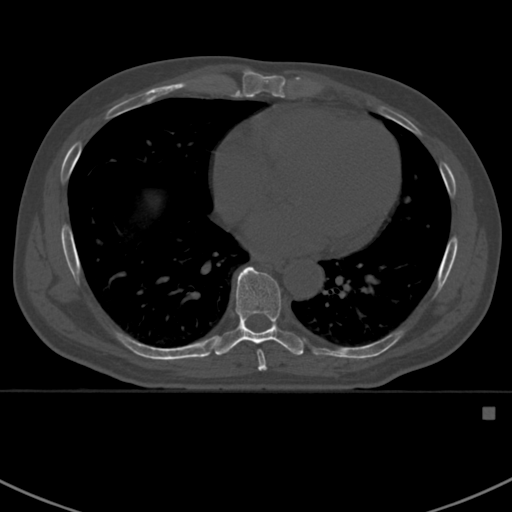
CT including the spine, one axial slice. Reconstruction kernel Br40s. 120 kVp. Bone window (W 1800 / L 400 HU). 512 × 512 image matrix, field of view 358 × 358 mm. Male patient, age 59 years. From the clinical record (not read from this slice): primary cancer: prostate.
Structures marked on this image (semi-automatically segmented with operator editing):
- T7 vertebra: bounding box <257,350,267,371> (left, top, right, bottom; pixels)
- T8 vertebra: <214,266,304,355>